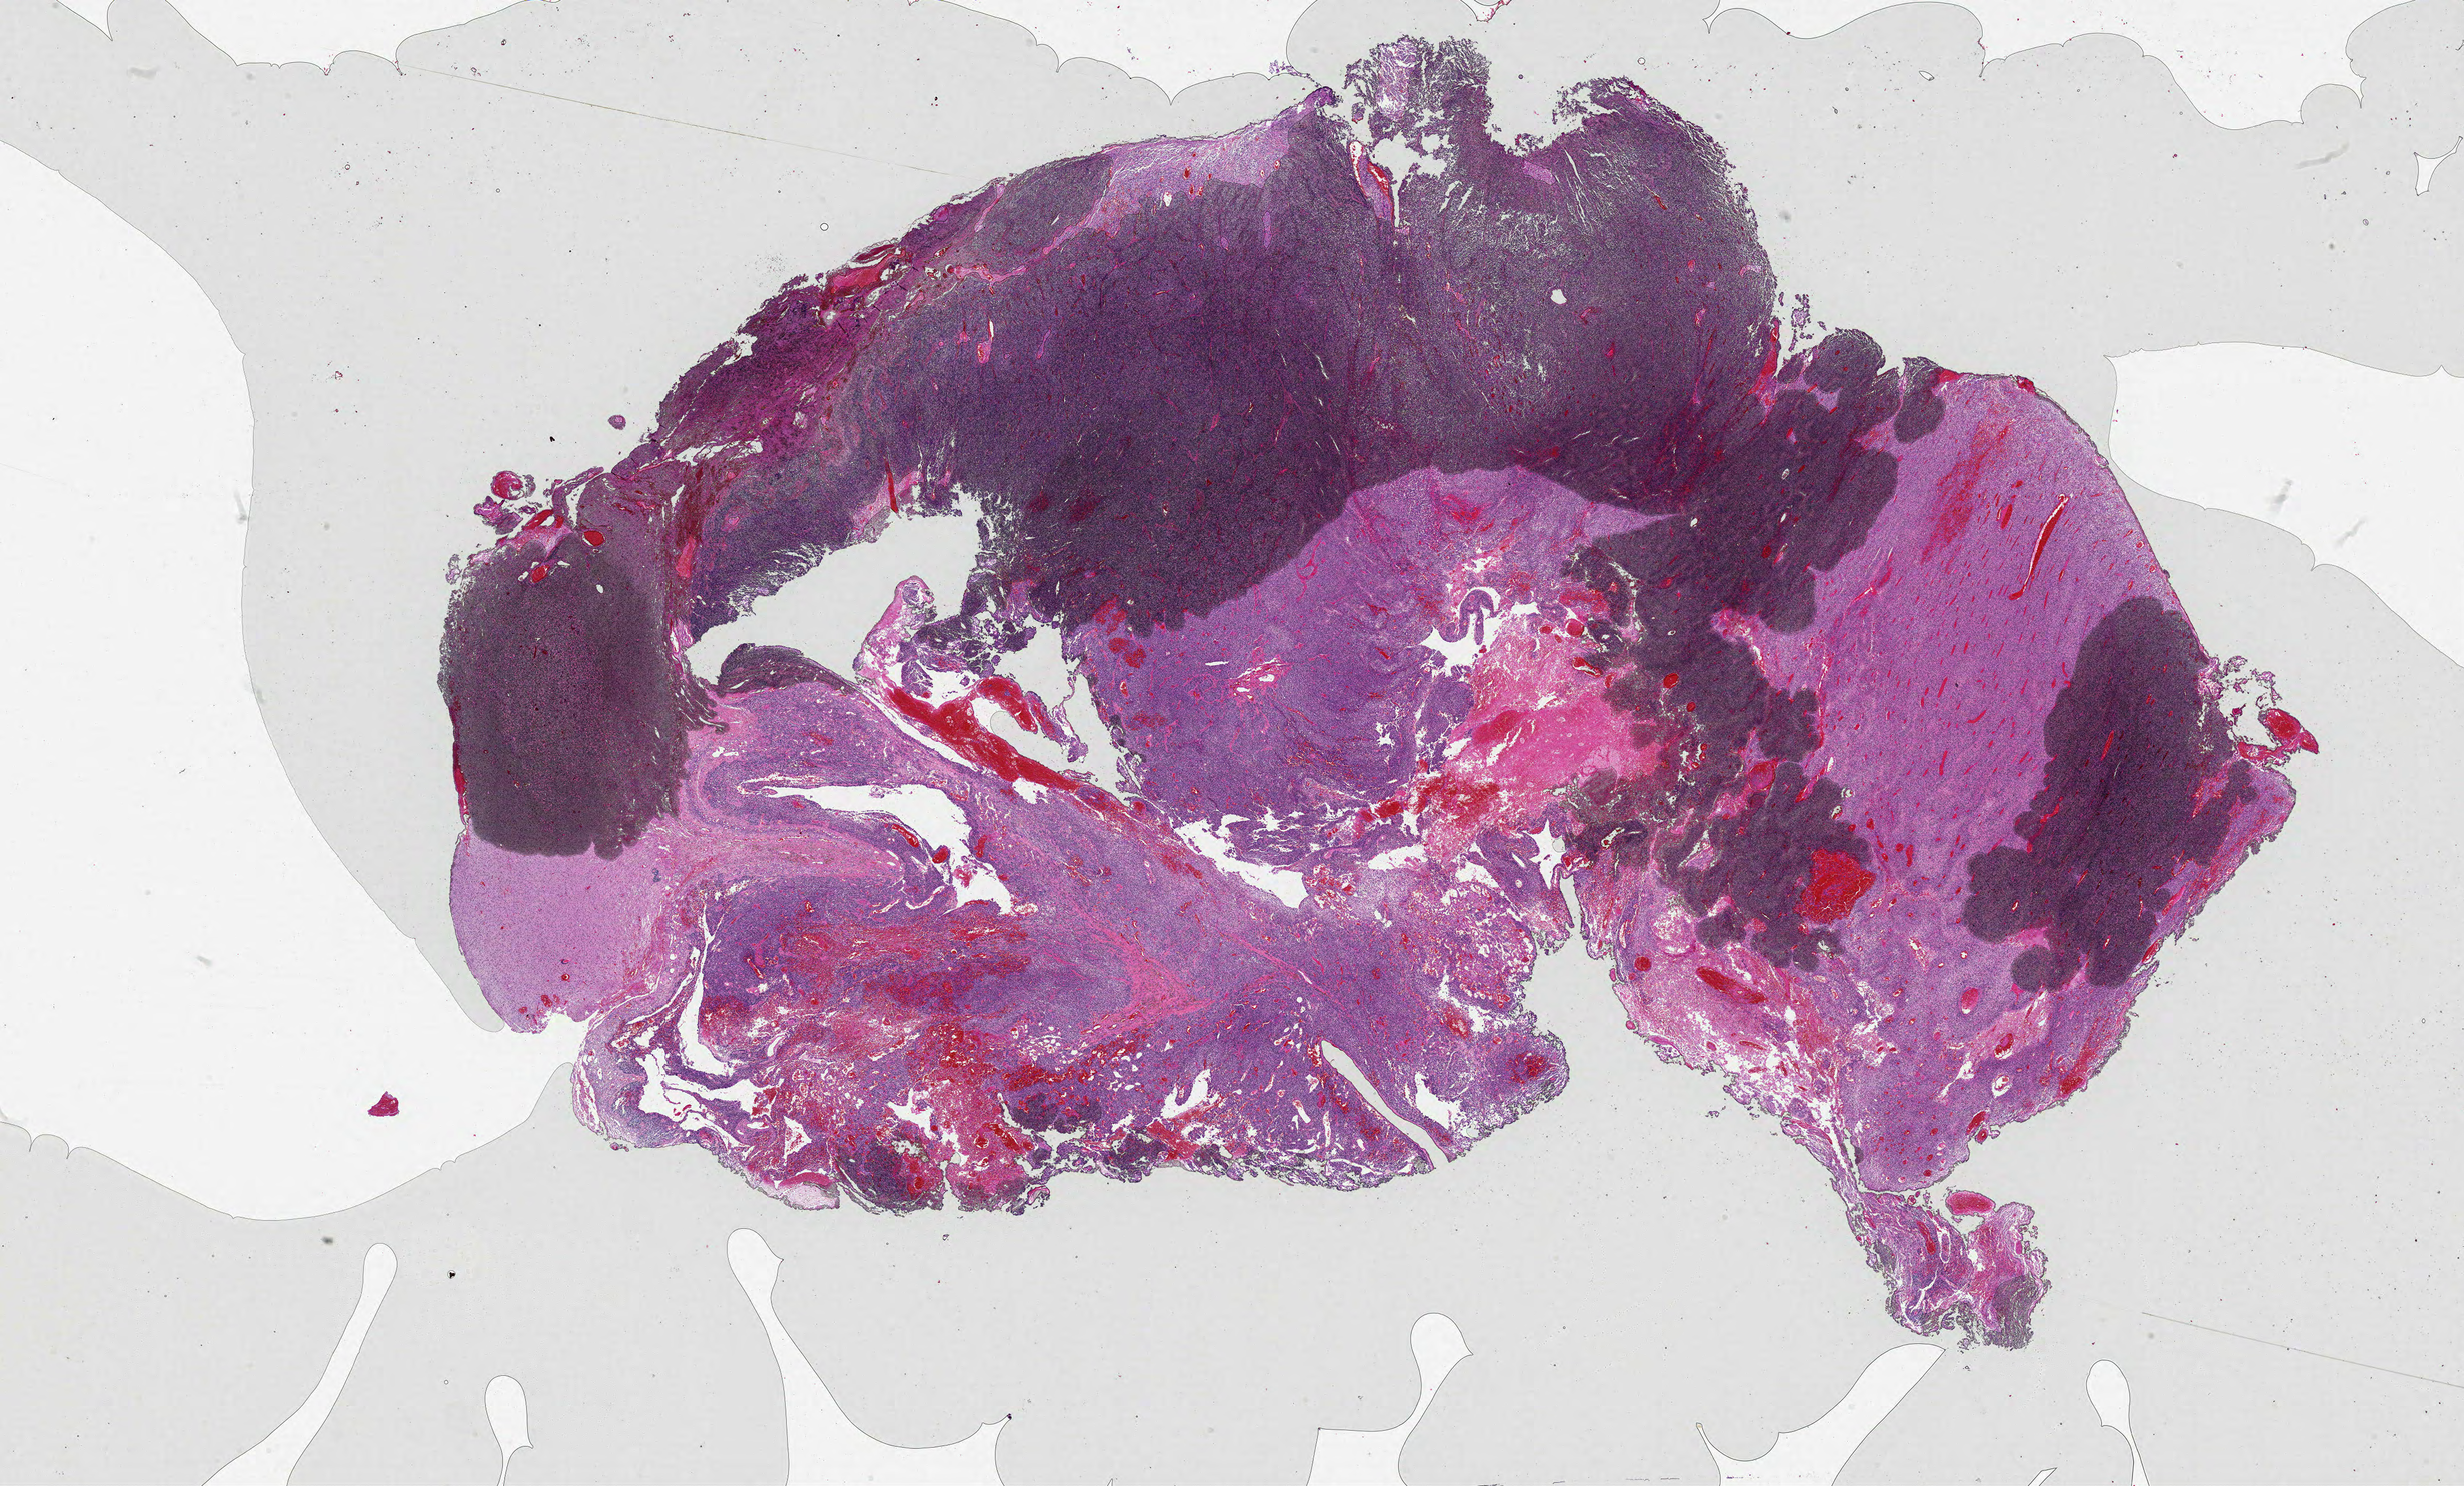
Whole-slide histology image, Hematoxylin and eosin (H&E) stained, low-resolution overview of the scanned area, about 37.0 x 22.3 mm, formalin-fixed paraffin-embedded (FFPE) diagnostic section, sample: primary tumour, brain. Male, age 52 years at initial diagnosis.
Histologic diagnosis: Glioblastoma.